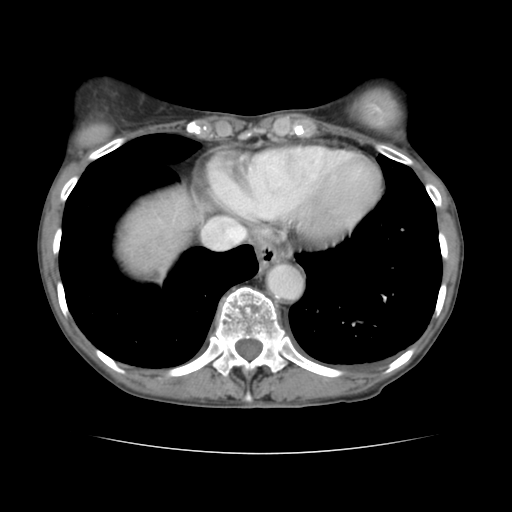
Contrast-enhanced abdominal CT, one axial slice. Slice 131 of 136 in the series (ordered by position). Intravenous contrast given. Soft-tissue window (W 400 / L 40 HU). 2.5 mm slice thickness. 512 × 512 image matrix, field of view 319 × 319 mm. Female patient, age 77 years. Case-level facts recorded for this patient, not image findings: diagnosis: colorectal cancer liver metastases, imaged before liver resection; multiple liver metastases: yes; largest metastasis: 3 cm.
Structures marked on this image (outlined manually by an expert reader):
- hepatic veins: bounding box <202,218,246,249> (left, top, right, bottom; pixels)
- liver: <116,189,193,276>